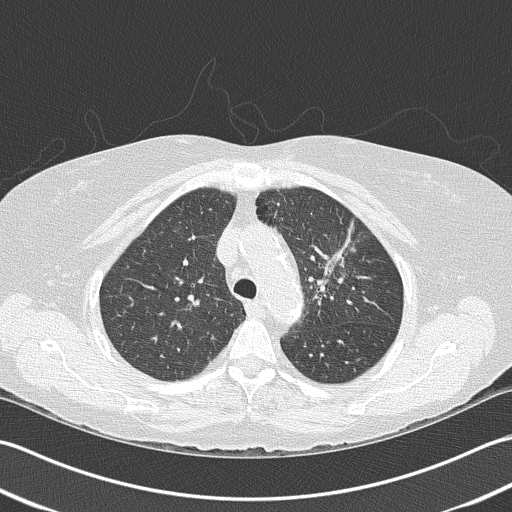
Low-dose screening chest CT, axial slice; baseline annual screen; lung window (W 1500 / L -600 HU); 2 mm slice thickness; lung (sharp) reconstruction kernel (B50f); 120 kVp. Female participant, aged 68 years at enrolment. Former smoker at enrolment.
Expert reader's lesion annotation, bounding box (x1, y1, x2, y2) in pixels: (297, 218, 372, 305). Screening reader's record for this exam: no non-calcified nodule ≥4 mm recorded. Official screen result: negative screen, minor abnormalities not suspicious for lung cancer. Participant outcome: lung cancer diagnosed 763 days after this screen (after the third annual screen) — adenocarcinoma, NOS, left upper lobe, poorly differentiated (G3), stage IB (AJCC 6th edition), 50 mm at pathology.